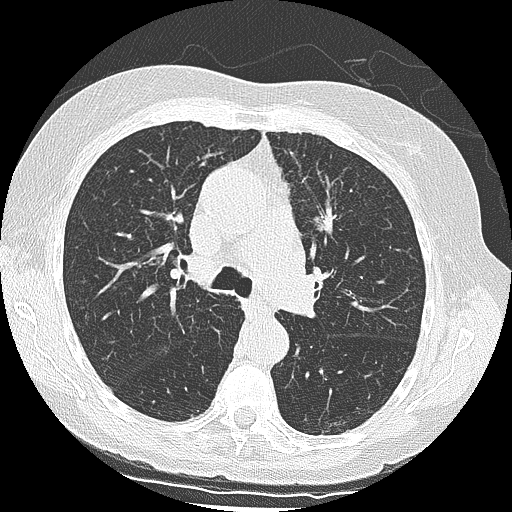
Low-dose screening chest CT, one axial slice. Position 92 of 139 along the scan axis. Lung window (W 1500 / L -600 HU). 2.5 mm slice thickness. 512 × 512 image matrix.
Outlined on this slice (expert manual segmentation):
- lesion 1 (tumor, upper lobe of left lung): box from (x=313, y=204) to (x=341, y=236) px